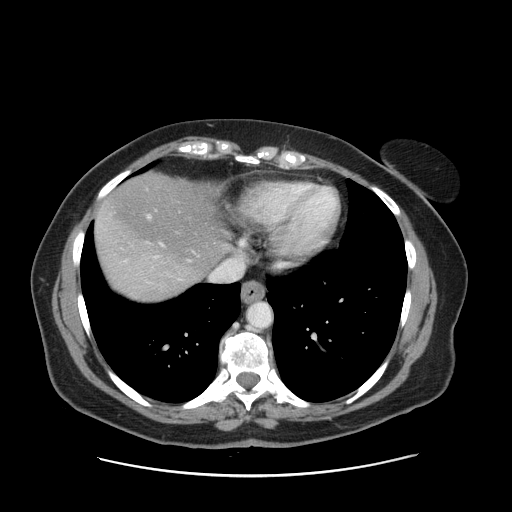
Contrast-enhanced abdominal CT, one axial slice; slice 139 of 161 in the series (ordered by position); 120 kVp; intravenous contrast given; soft-tissue window (W 400 / L 40 HU); 2.5 mm slice thickness; 512 × 512 image matrix. Female patient, age 62 years. From the clinical record (not read from this slice): diagnosis: colorectal cancer liver metastases, imaged before liver resection.
Outlined on this slice (expert manual segmentation):
- hepatic veins: box from (x=145, y=187) to (x=243, y=280) px
- liver: (x=96, y=174)–(x=225, y=301)
- planned liver remnant (the part of the liver to remain after resection): (x=98, y=174)–(x=226, y=274)
- portal vein (with intrahepatic branches): (x=149, y=216)–(x=151, y=218)